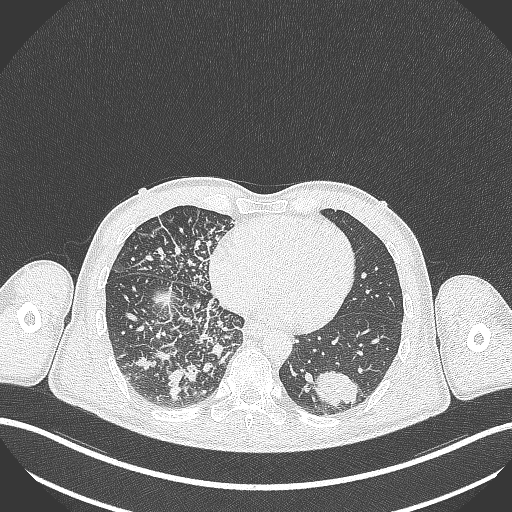
Chest CT, one axial slice. Position 105 of 348 along the scan axis. Lung window (W 1500 / L -600 HU). 1 mm slice thickness. 512 × 512 image matrix. Male patient, age 49 years. From the clinical record (not read from this slice): clinical TNM (as recorded): T2b N1 M0.
Structures marked on this image (bounding box drawn by a radiologist):
- lung tumour (recorded histology: adenocarcinoma): bounding box [x1, y1, x2, y2] px = [314, 368, 363, 407]